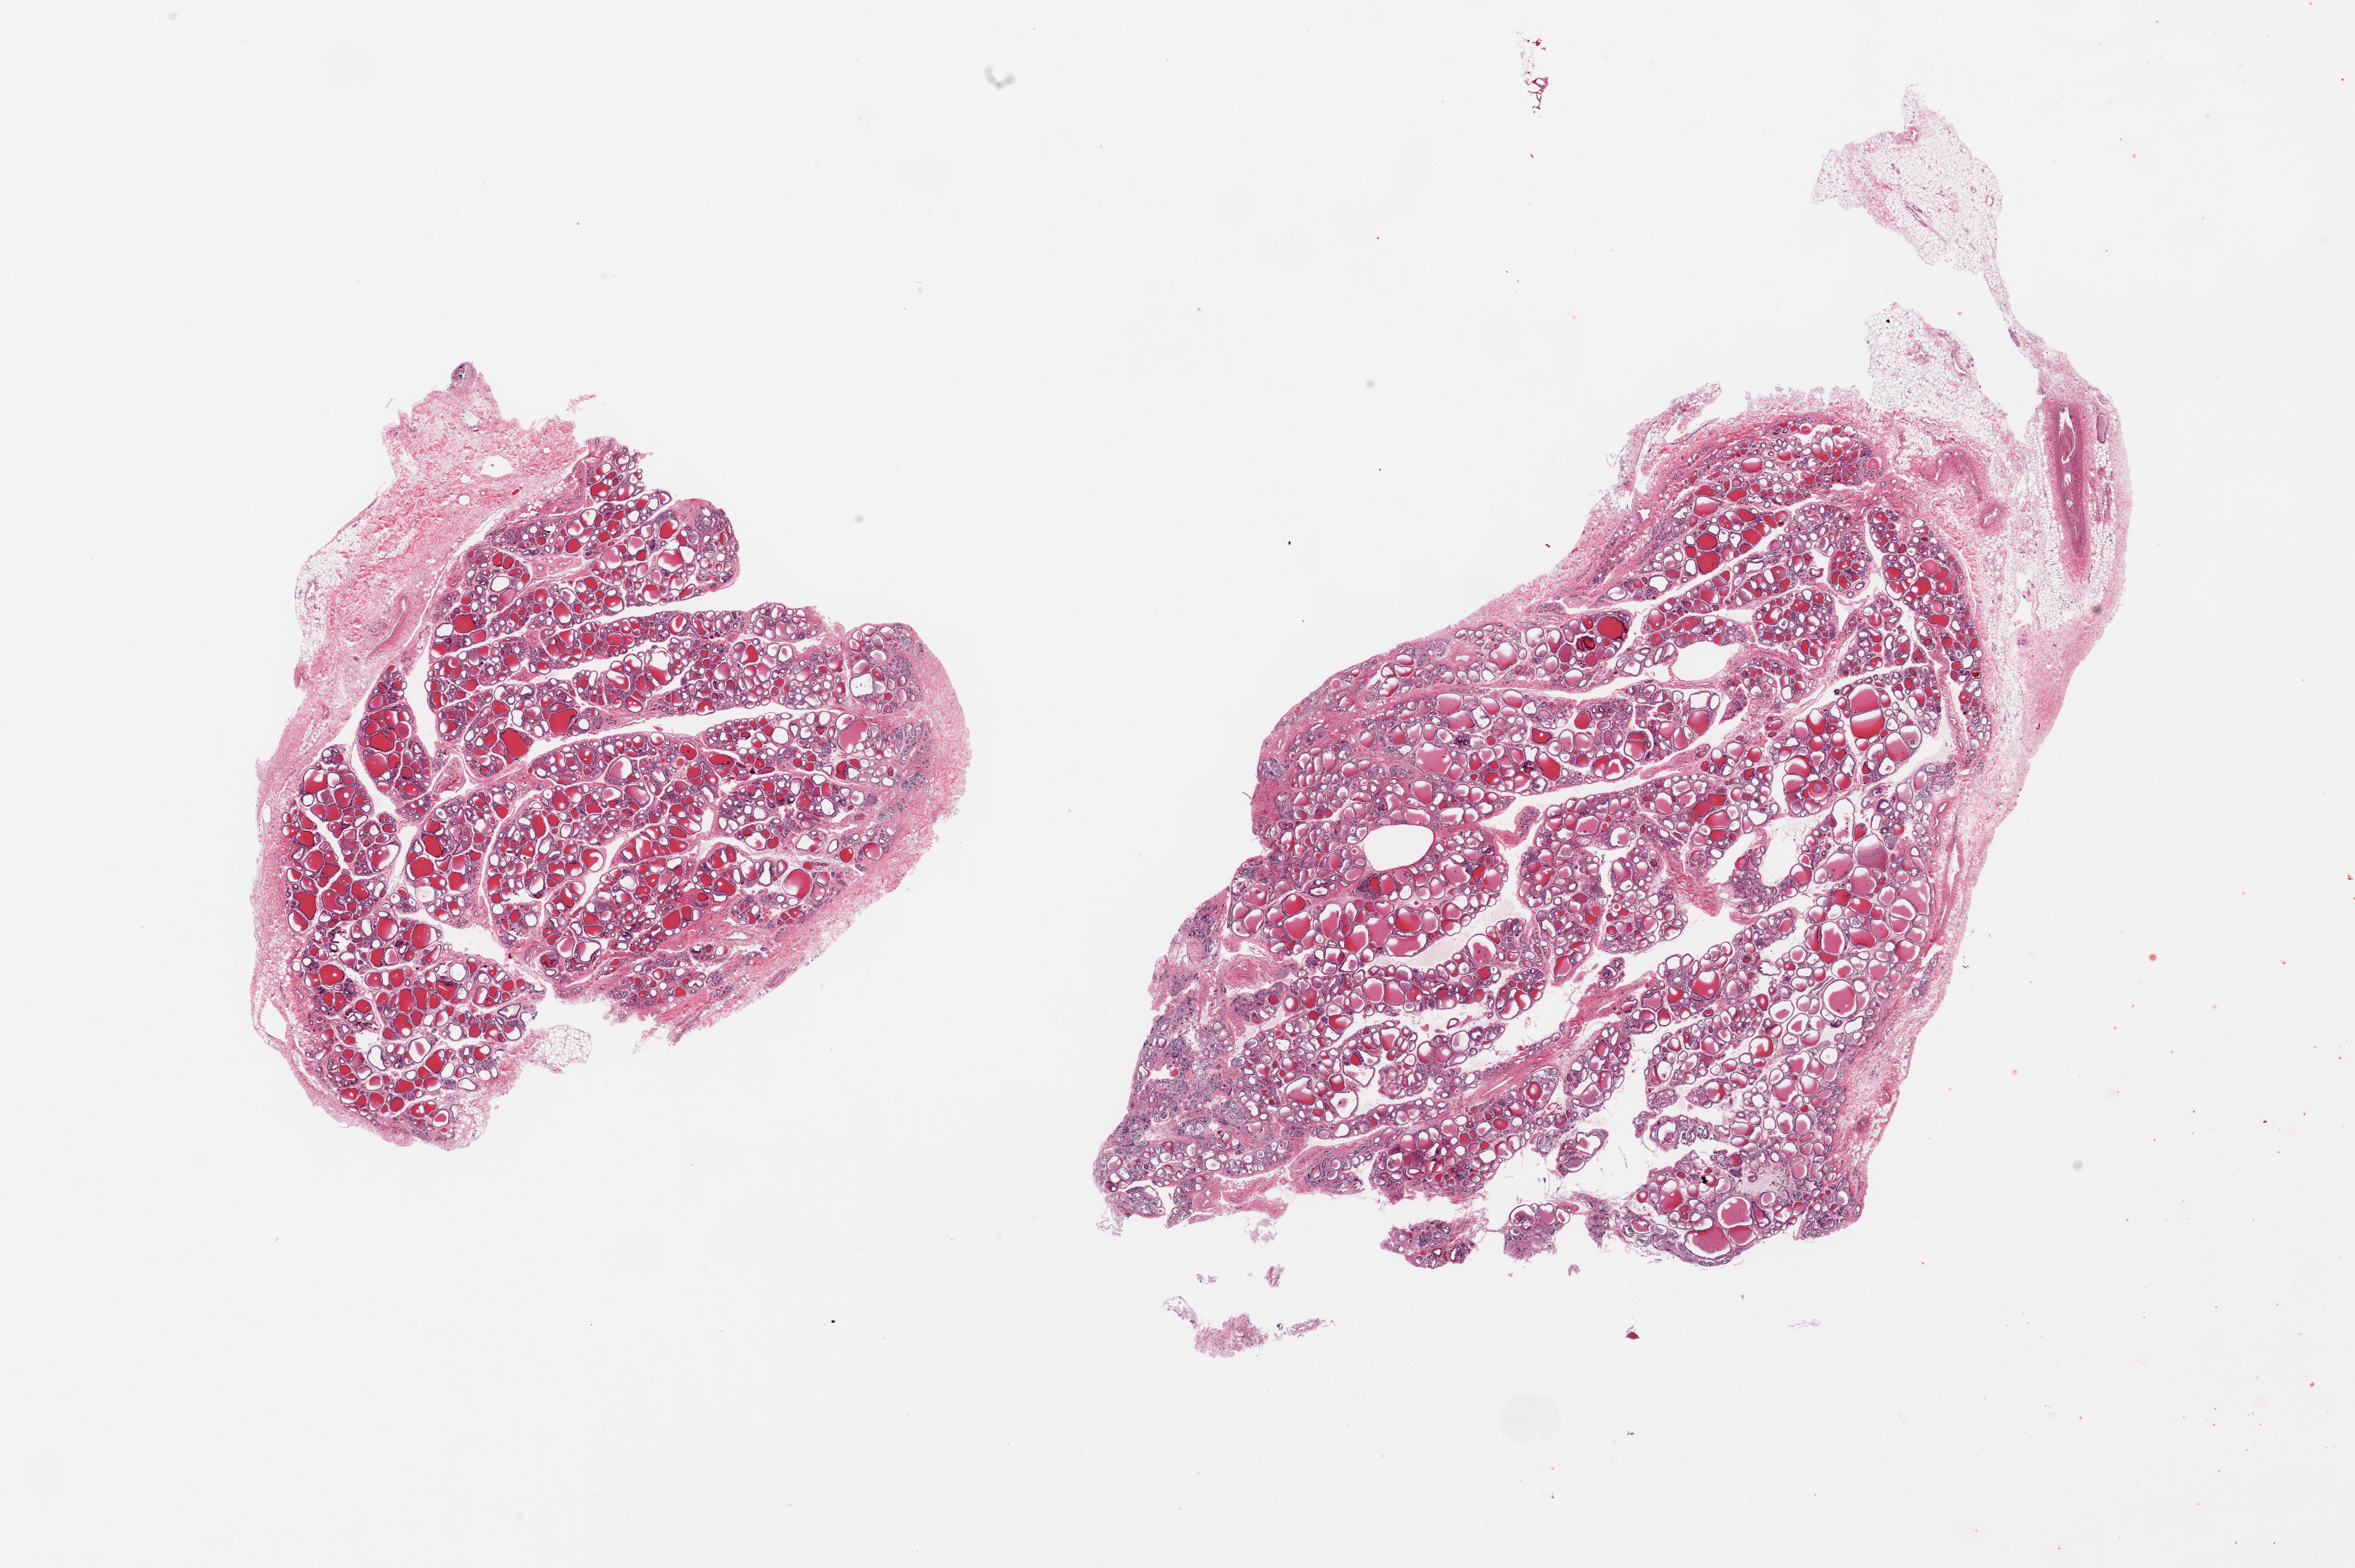
Whole-slide image, hematoxylin and eosin (H&E) stain, a low-resolution overview of the entire scanned area, about 25.6 x 17.0 mm (from a 20x scan); PAXgene-fixed paraffin-embedded (PFPE) section; section of thyroid (target tissue); tissue donor sample. Male donor.
Reviewer comment on this tissue sample: 2 pieces; both include ~10% fat/vessels/connective tissue, mild to moderate autolysis.